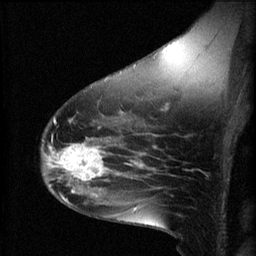
Breast MRI (dynamic contrast-enhanced), one sagittal slice; slice 38 of 60 in the series (ordered by position); 3 images stored at this slice position (order not interpretable as contrast timing); 1.5 T; TE 4.2 ms, TR 8.2 ms; 2 mm slice thickness; 256 × 256 image matrix, field of view 180 × 180 mm. Patient: female, 49 years.
Annotated regions visible in this slice (semi-automatically segmented with operator editing):
- analysis volume of interest (the breast-tissue region the enhancement analysis was run in; not a lesion): box from (x=45, y=136) to (x=109, y=187) px
- tumour enhancement mask (voxels above the 70 % enhancement threshold inside the analysis volume of interest): (x=45, y=140)–(x=109, y=187)